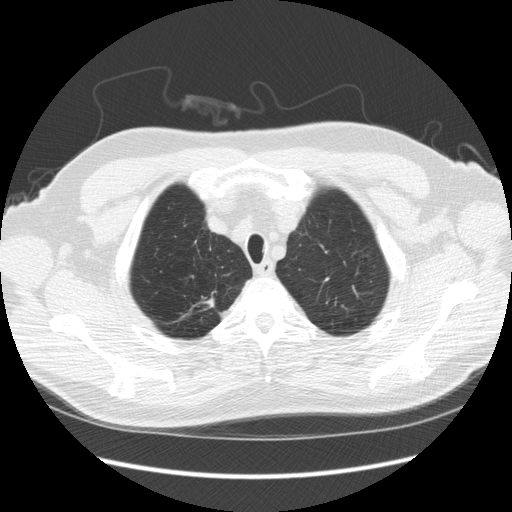
Axial slice from a low-dose chest CT screening exam, third annual screen, lung window (W 1500 / L -600 HU), 2.5 mm slice thickness, slice 28 of 248 in the series. Male participant, aged 64 years at enrolment. Former smoker at enrolment.
Expert reader's lesion annotation, bounding box (x1, y1, x2, y2) in pixels: (182, 286, 227, 323). The screening reader recorded 4 non-calcified nodules or masses ≥4 mm on this exam (right upper lobe, right upper lobe, right upper lobe, right upper lobe); which of them this box marks is not recorded. Official screen result: positive, other. Later outcome: lung cancer diagnosed 15 days after this screen — adenocarcinoma, NOS, right upper lobe, moderately differentiated (G2), stage IA (AJCC 6th edition), 14 mm at pathology.